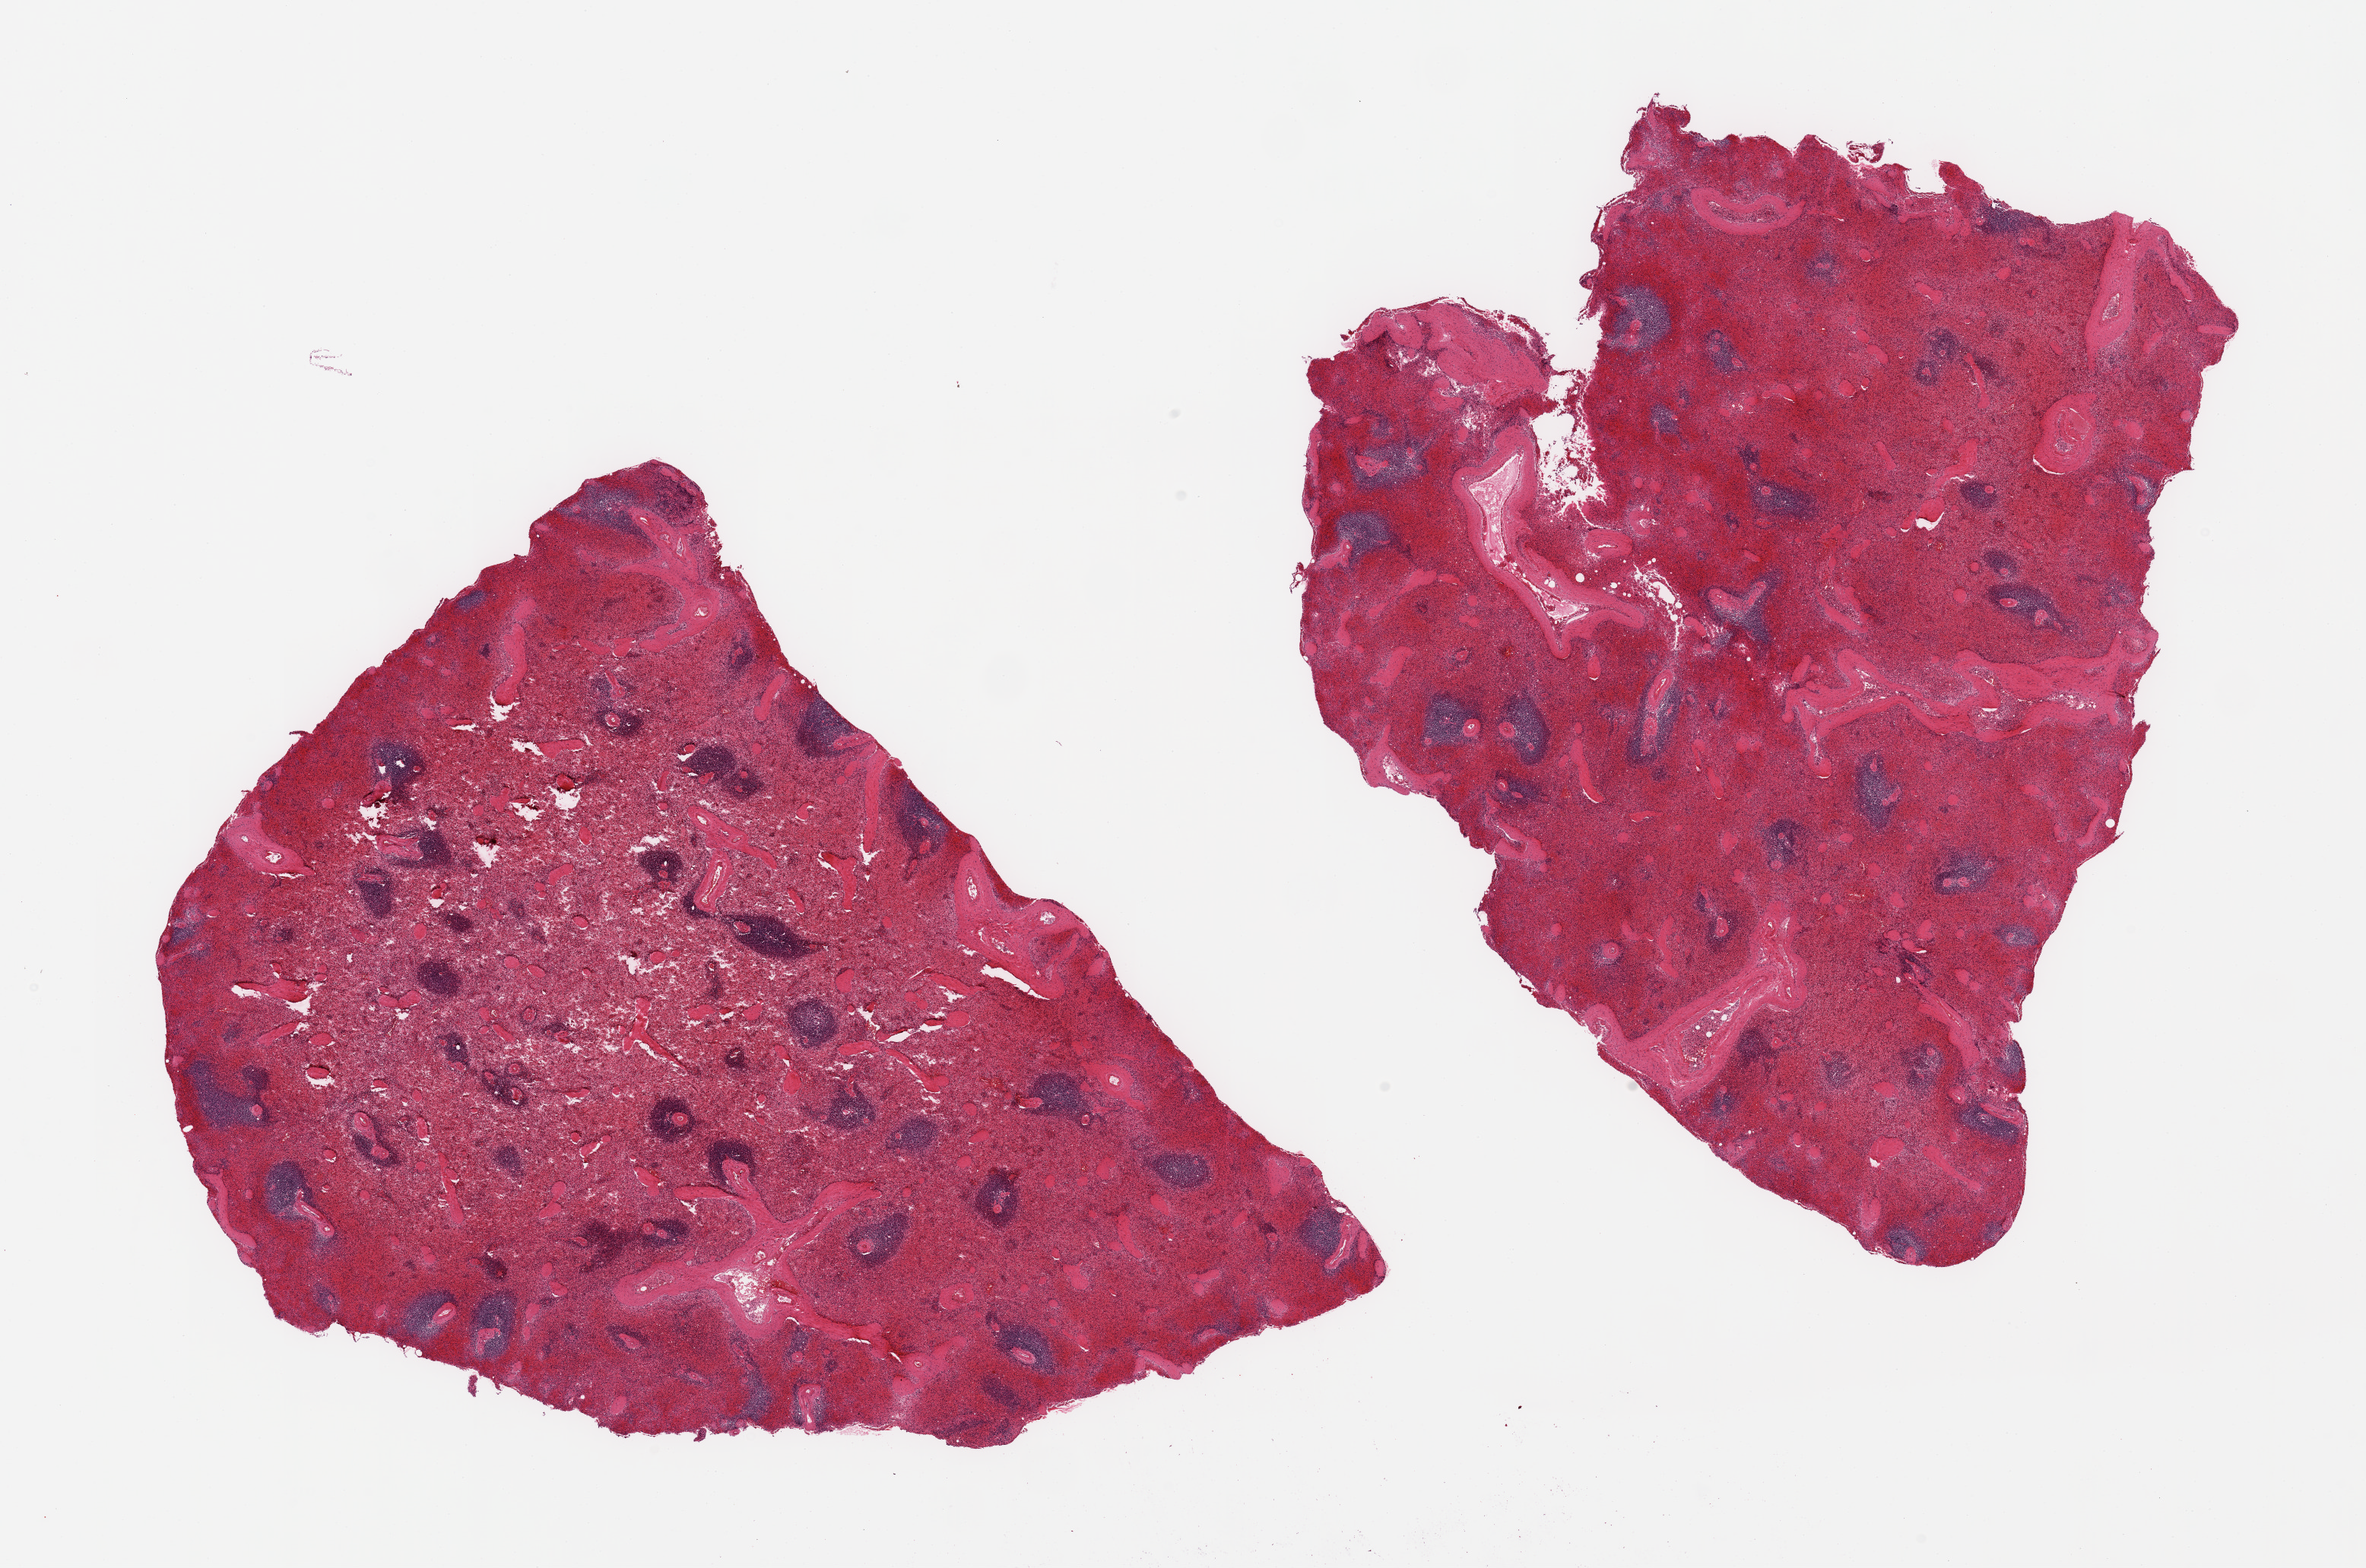
Hematoxylin and eosin (H&E) whole-slide image, a low-resolution overview of the entire scanned area, about 24.6 x 16.3 mm, PAXgene-fixed paraffin-embedded (PFPE) section, section of spleen (target tissue), tissue donor sample. Donor sex: male.
Pathologist's review note for this sample: 2 pieces, moderate congestion.